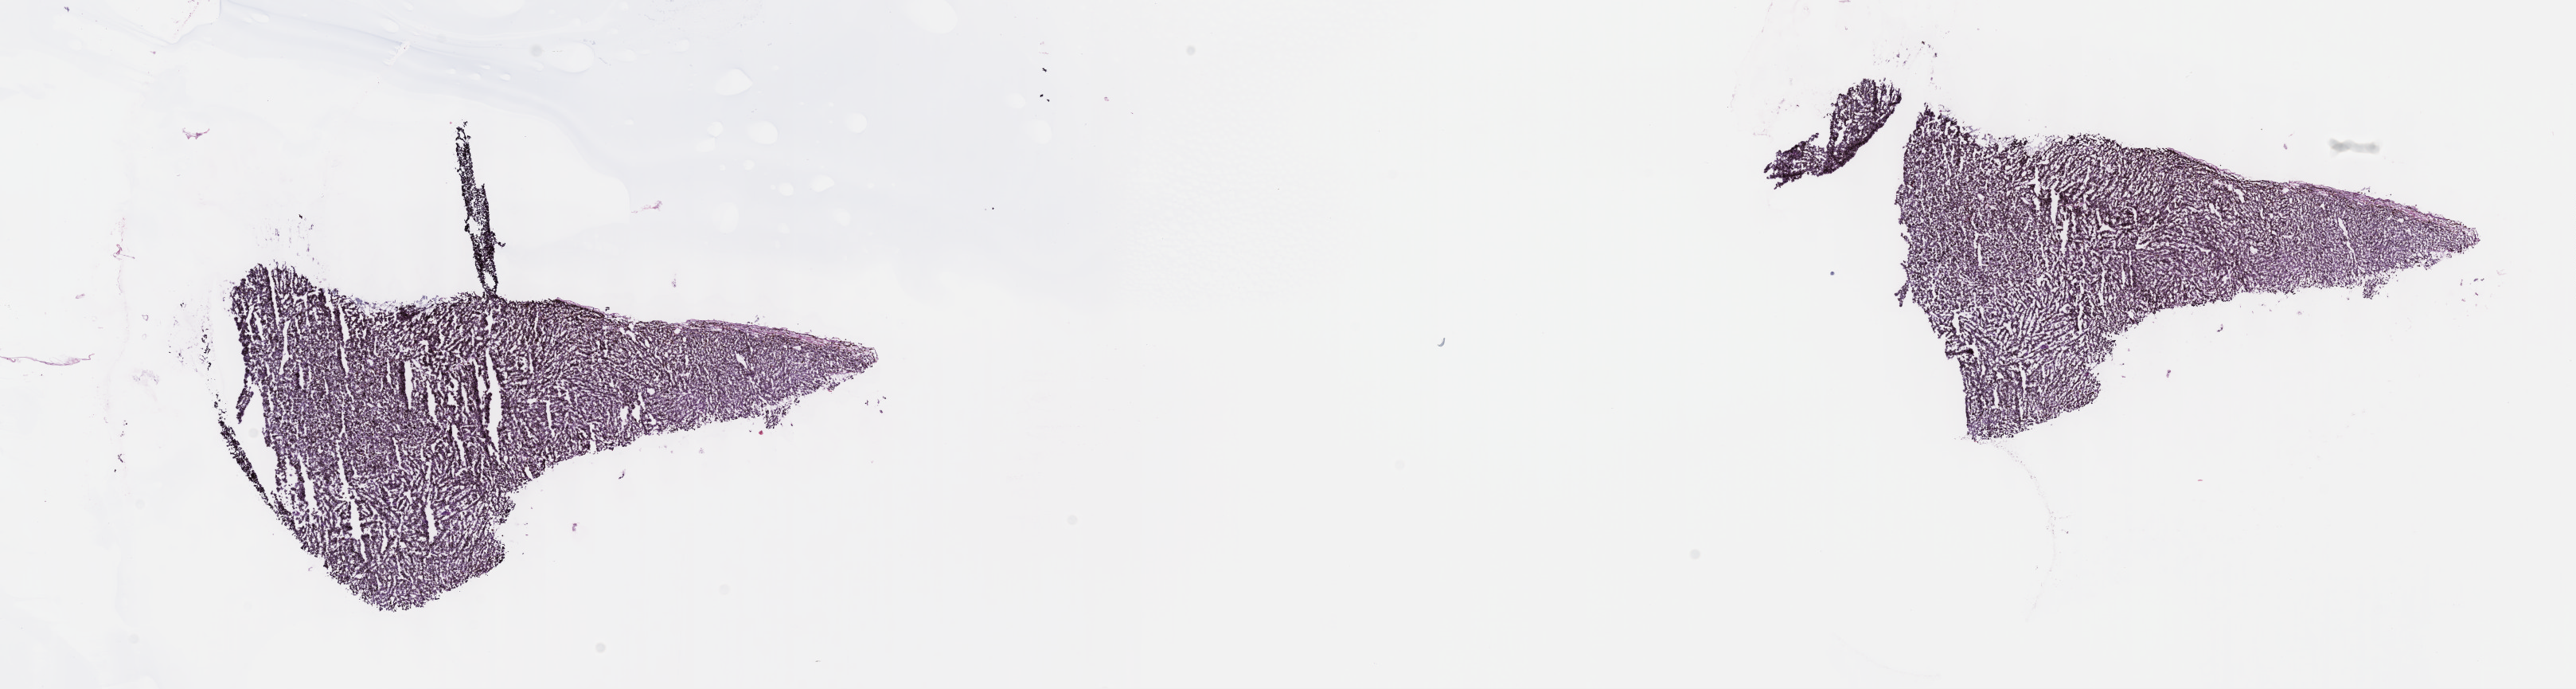
Digitized H&E tissue section (whole slide), shown as a low-resolution overview of the whole scanned area (about 26.2 x 7.0 mm, from a 40x scan). Frozen section. Sample: primary tumour, uvea. Male patient; age at initial diagnosis 68 years. Slide review estimates, as recorded: tumour cells 100%, tumour nuclei 80%, normal cells 0%, stromal cells 0%, necrosis 0%. Infiltration values recorded for this section: lymphocyte infiltration 1%, monocyte infiltration 0%, neutrophil infiltration 0%.
Histologic diagnosis: Mixed epithelioid and spindle cell melanoma (choroid). Laterality: right. AJCC pathologic stage: IIB (7th edition).